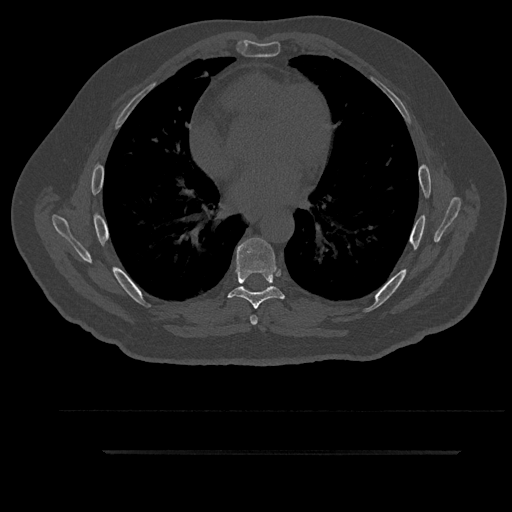
CT including the spine, one axial slice. Slice 531 of 797 in the series (ordered by position). Reconstruction kernel Br40s/3. 120 kVp. Bone window (W 1800 / L 400 HU). 512 × 512 image matrix. Patient: male, 63 years. From the clinical record (not read from this slice): primary cancer: renal.
Outlined on this slice (semi-automatic segmentation, software-assisted and operator-edited):
- T6 vertebra: bounding box (x1, y1, x2, y2) in pixels: (250, 315, 258, 325)
- T7 vertebra: (228, 237, 285, 309)